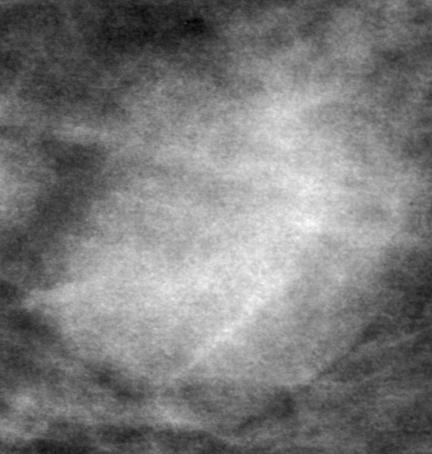
Crop from a digitized film mammogram around one marked abnormality; right breast; CC view; BI-RADS breast density category 3 (scale 1–4).
- Finding: mass, shape oval, margins obscured; BI-RADS assessment category 0 (incomplete: needs additional imaging); subtlety rating 5 on a 1 (subtle) to 5 (obvious) scale; pathology result (as recorded, not read from the image): benign.